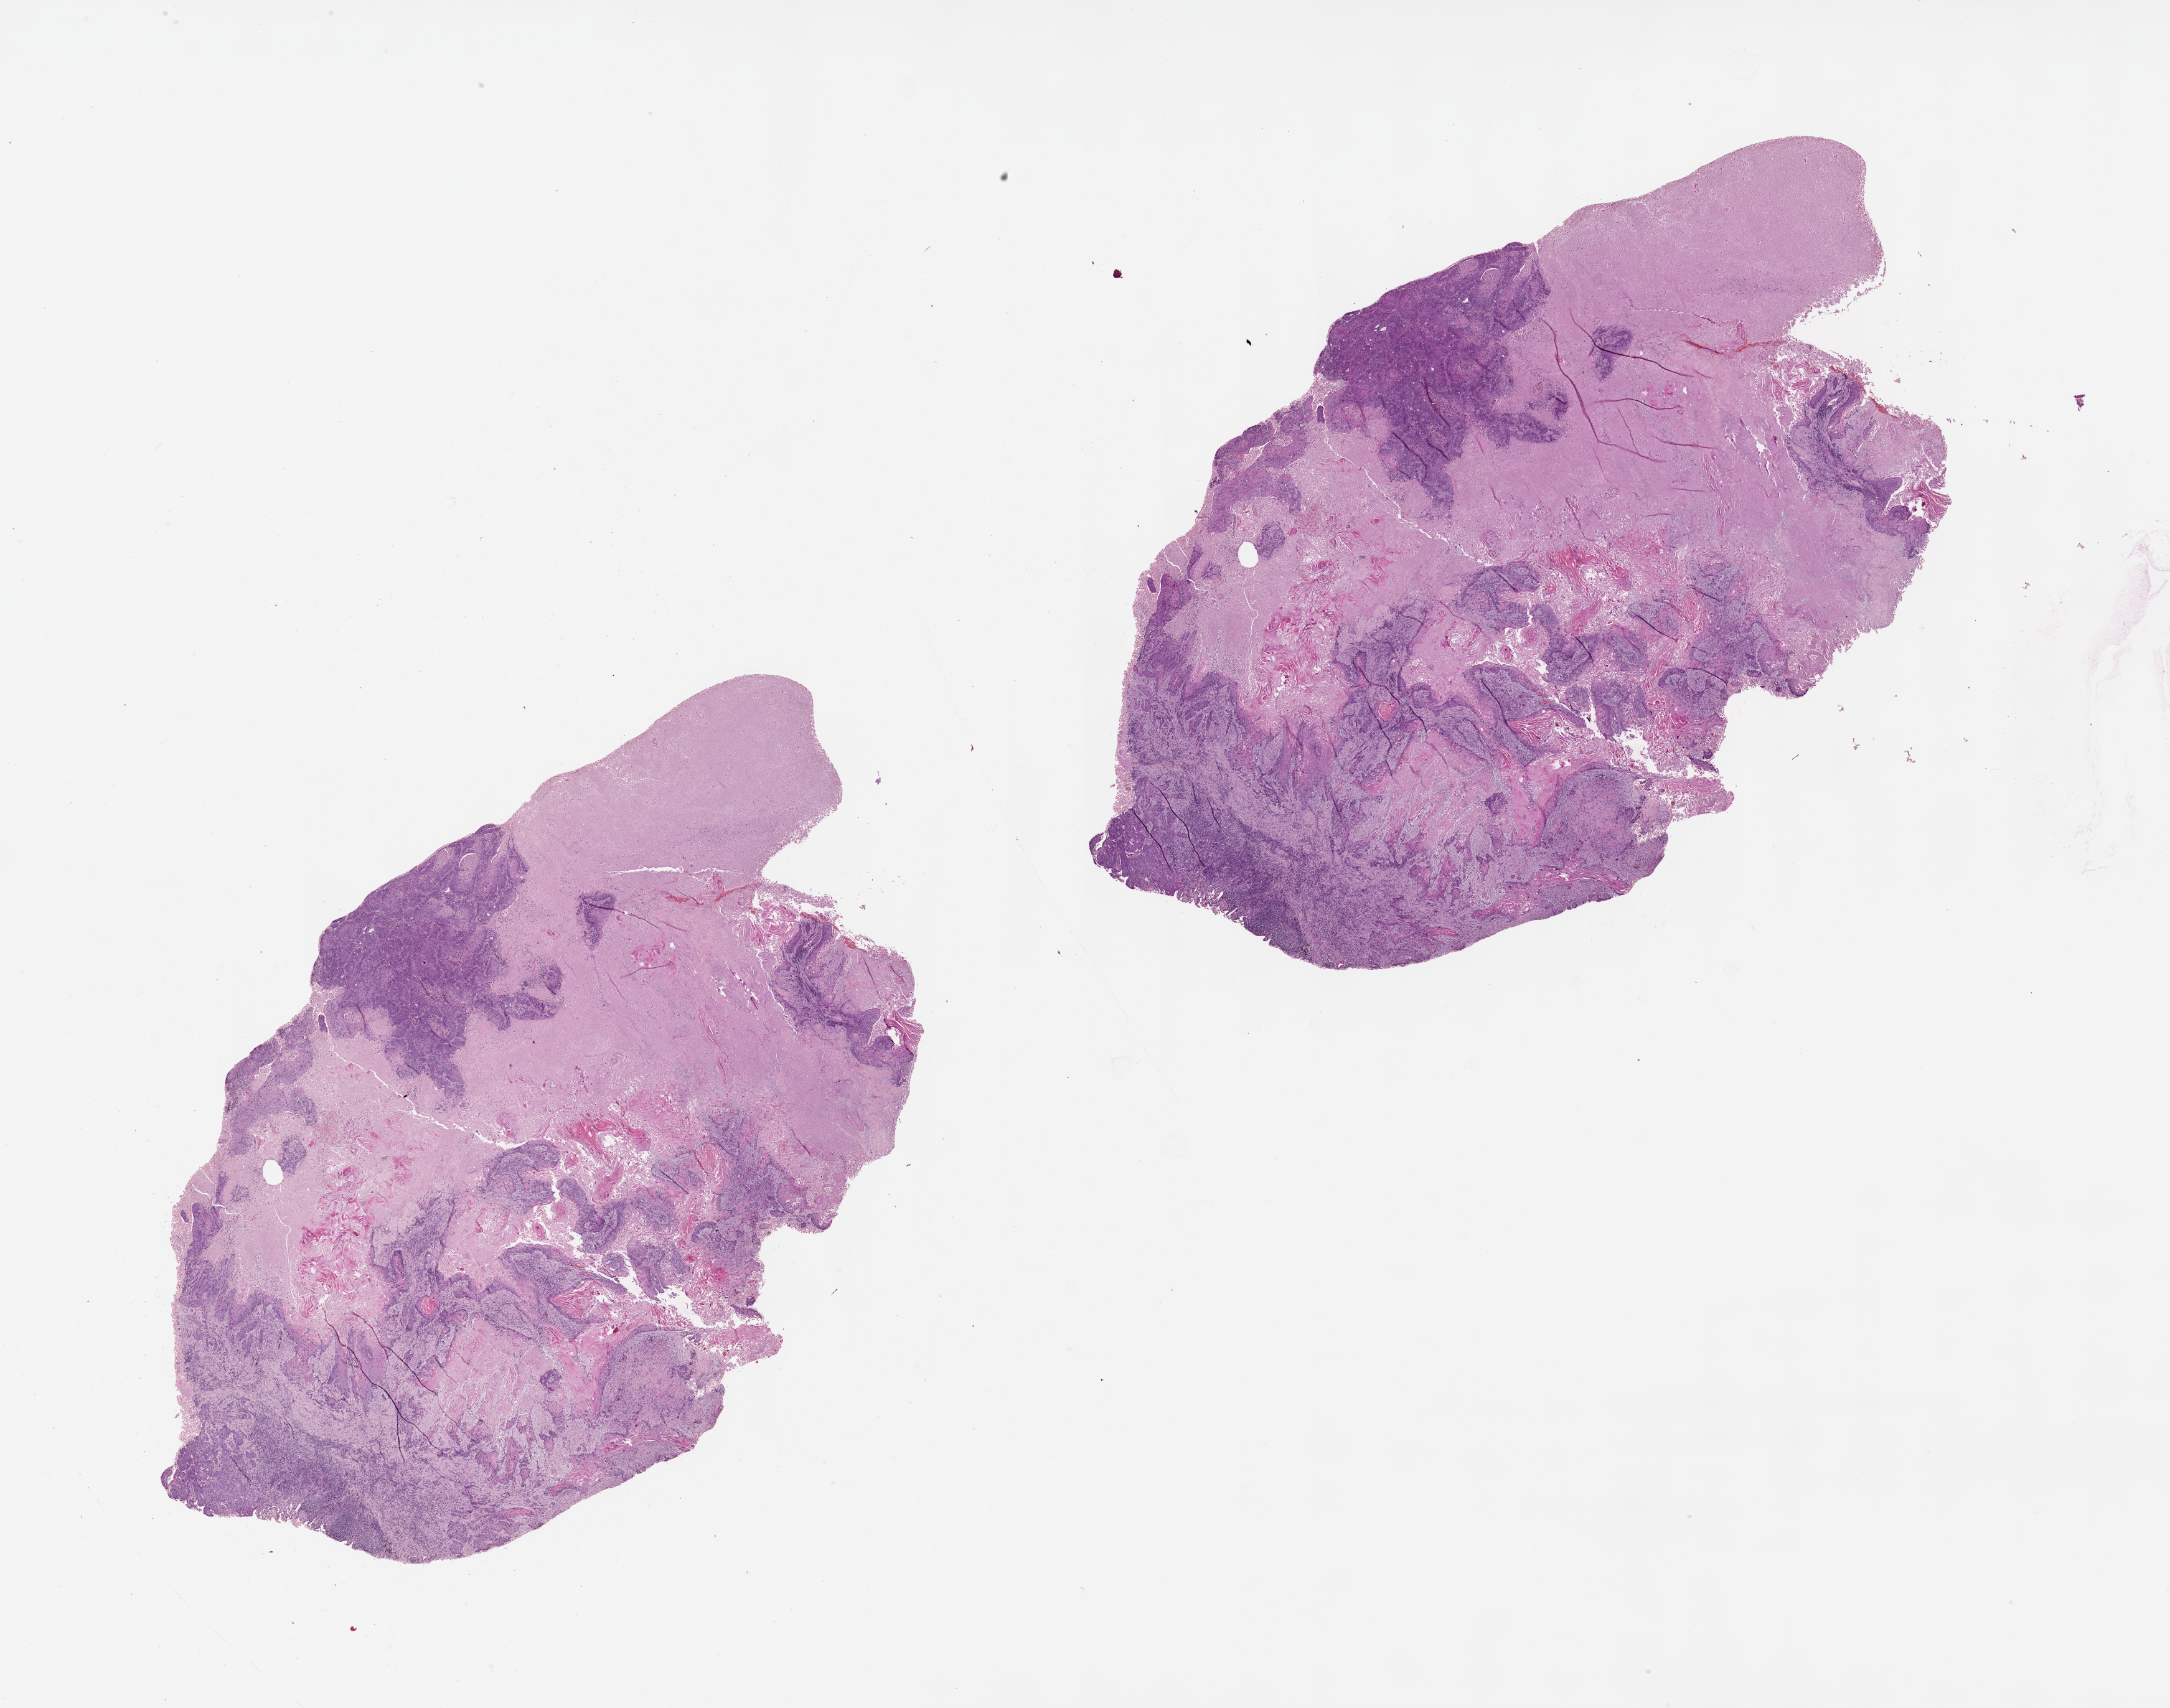
H&E whole-slide image — low-resolution overview of the scanned area, about 28.1 x 22.1 mm (slide scanned at 20x), lung, tumour tissue. 60-year-old female patient.
Patient diagnosis (cohort enrolment): squamous cell carcinoma (lung).